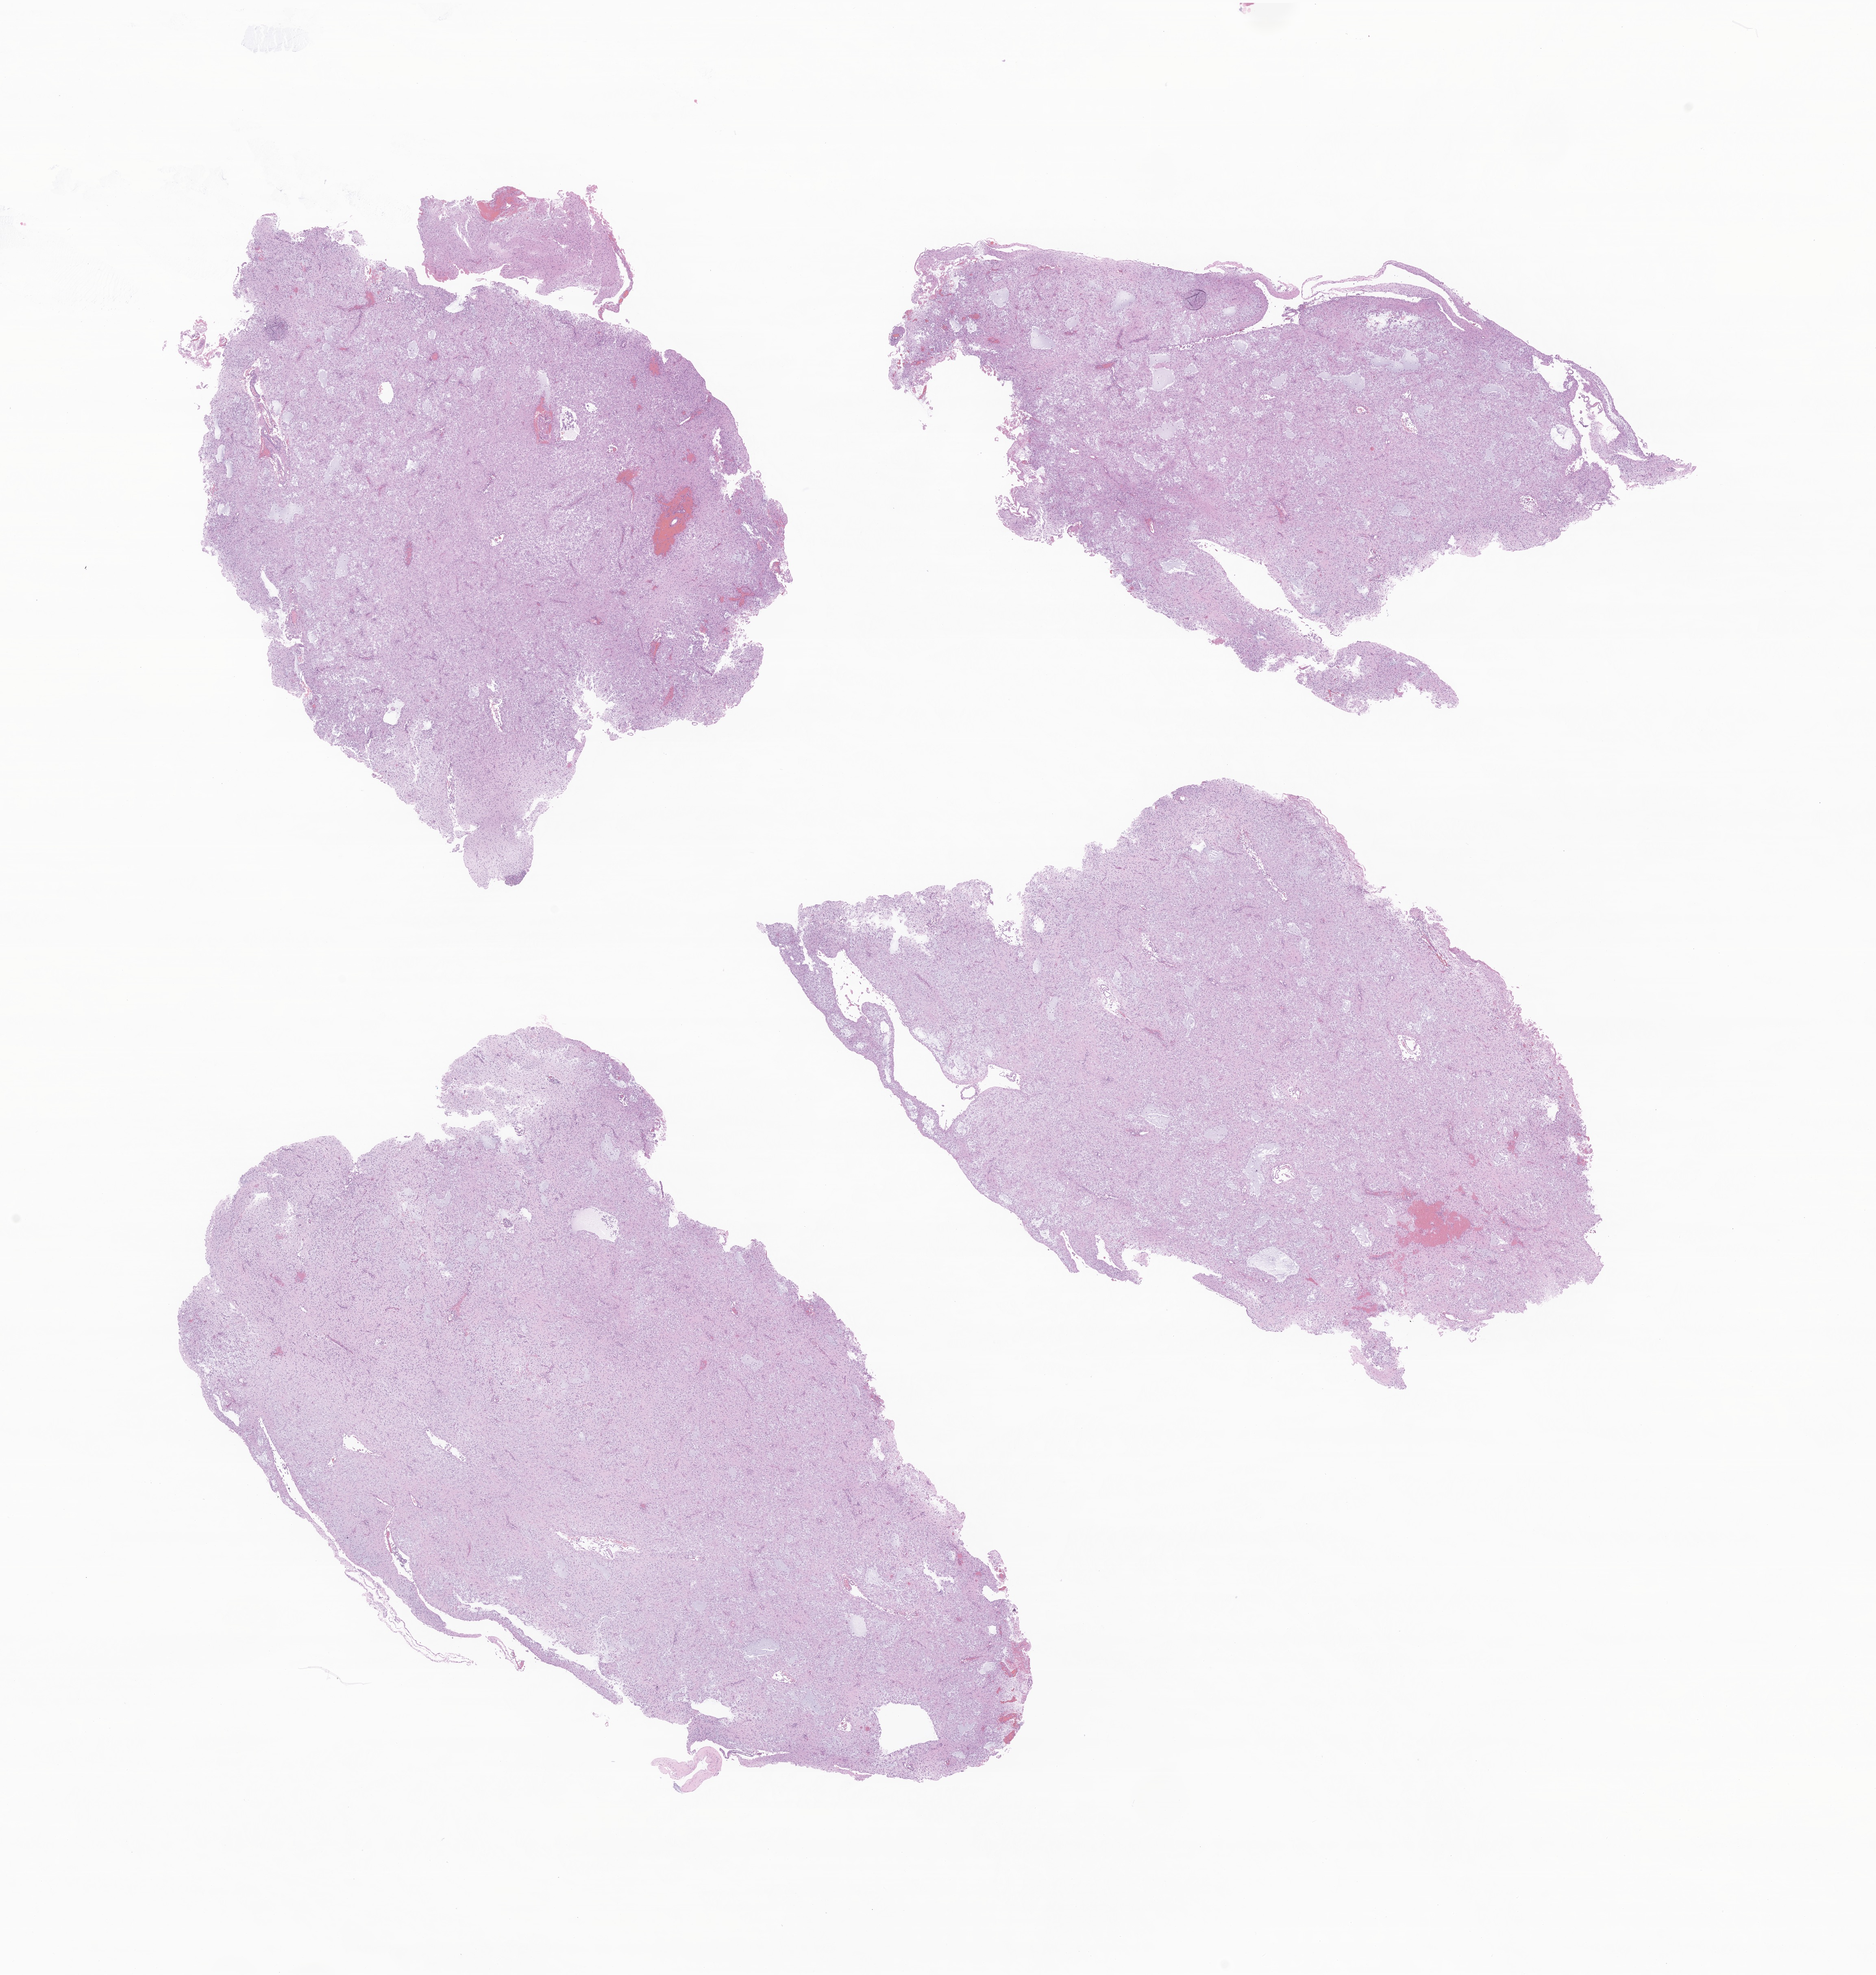
Whole-slide image, H&E stain of tumor tissue from the brain, low-resolution overview of the scanned area, about 19.4 x 20.5 mm, formalin-fixed paraffin-embedded section. Patient female; age 83 months.
• diagnosis: Pilocytic astrocytoma